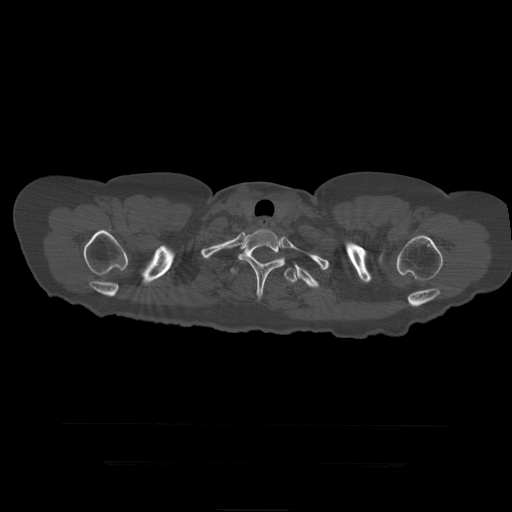
CT including the spine, one axial slice; slice 374 of 399 in the series (ordered by position); bone window (W 1800 / L 400 HU); 1.25 mm slice thickness; 512 × 512 image matrix. Patient age 41 years. From the clinical record (not read from this slice): primary cancer: breast.
Outlined on this slice (semi-automatically segmented with operator editing):
- T1 vertebra: bounding box [x1, y1, x2, y2] px = [254, 229, 267, 233]
- T2 vertebra: [238, 229, 286, 300]
- T3 vertebra: [231, 257, 298, 283]